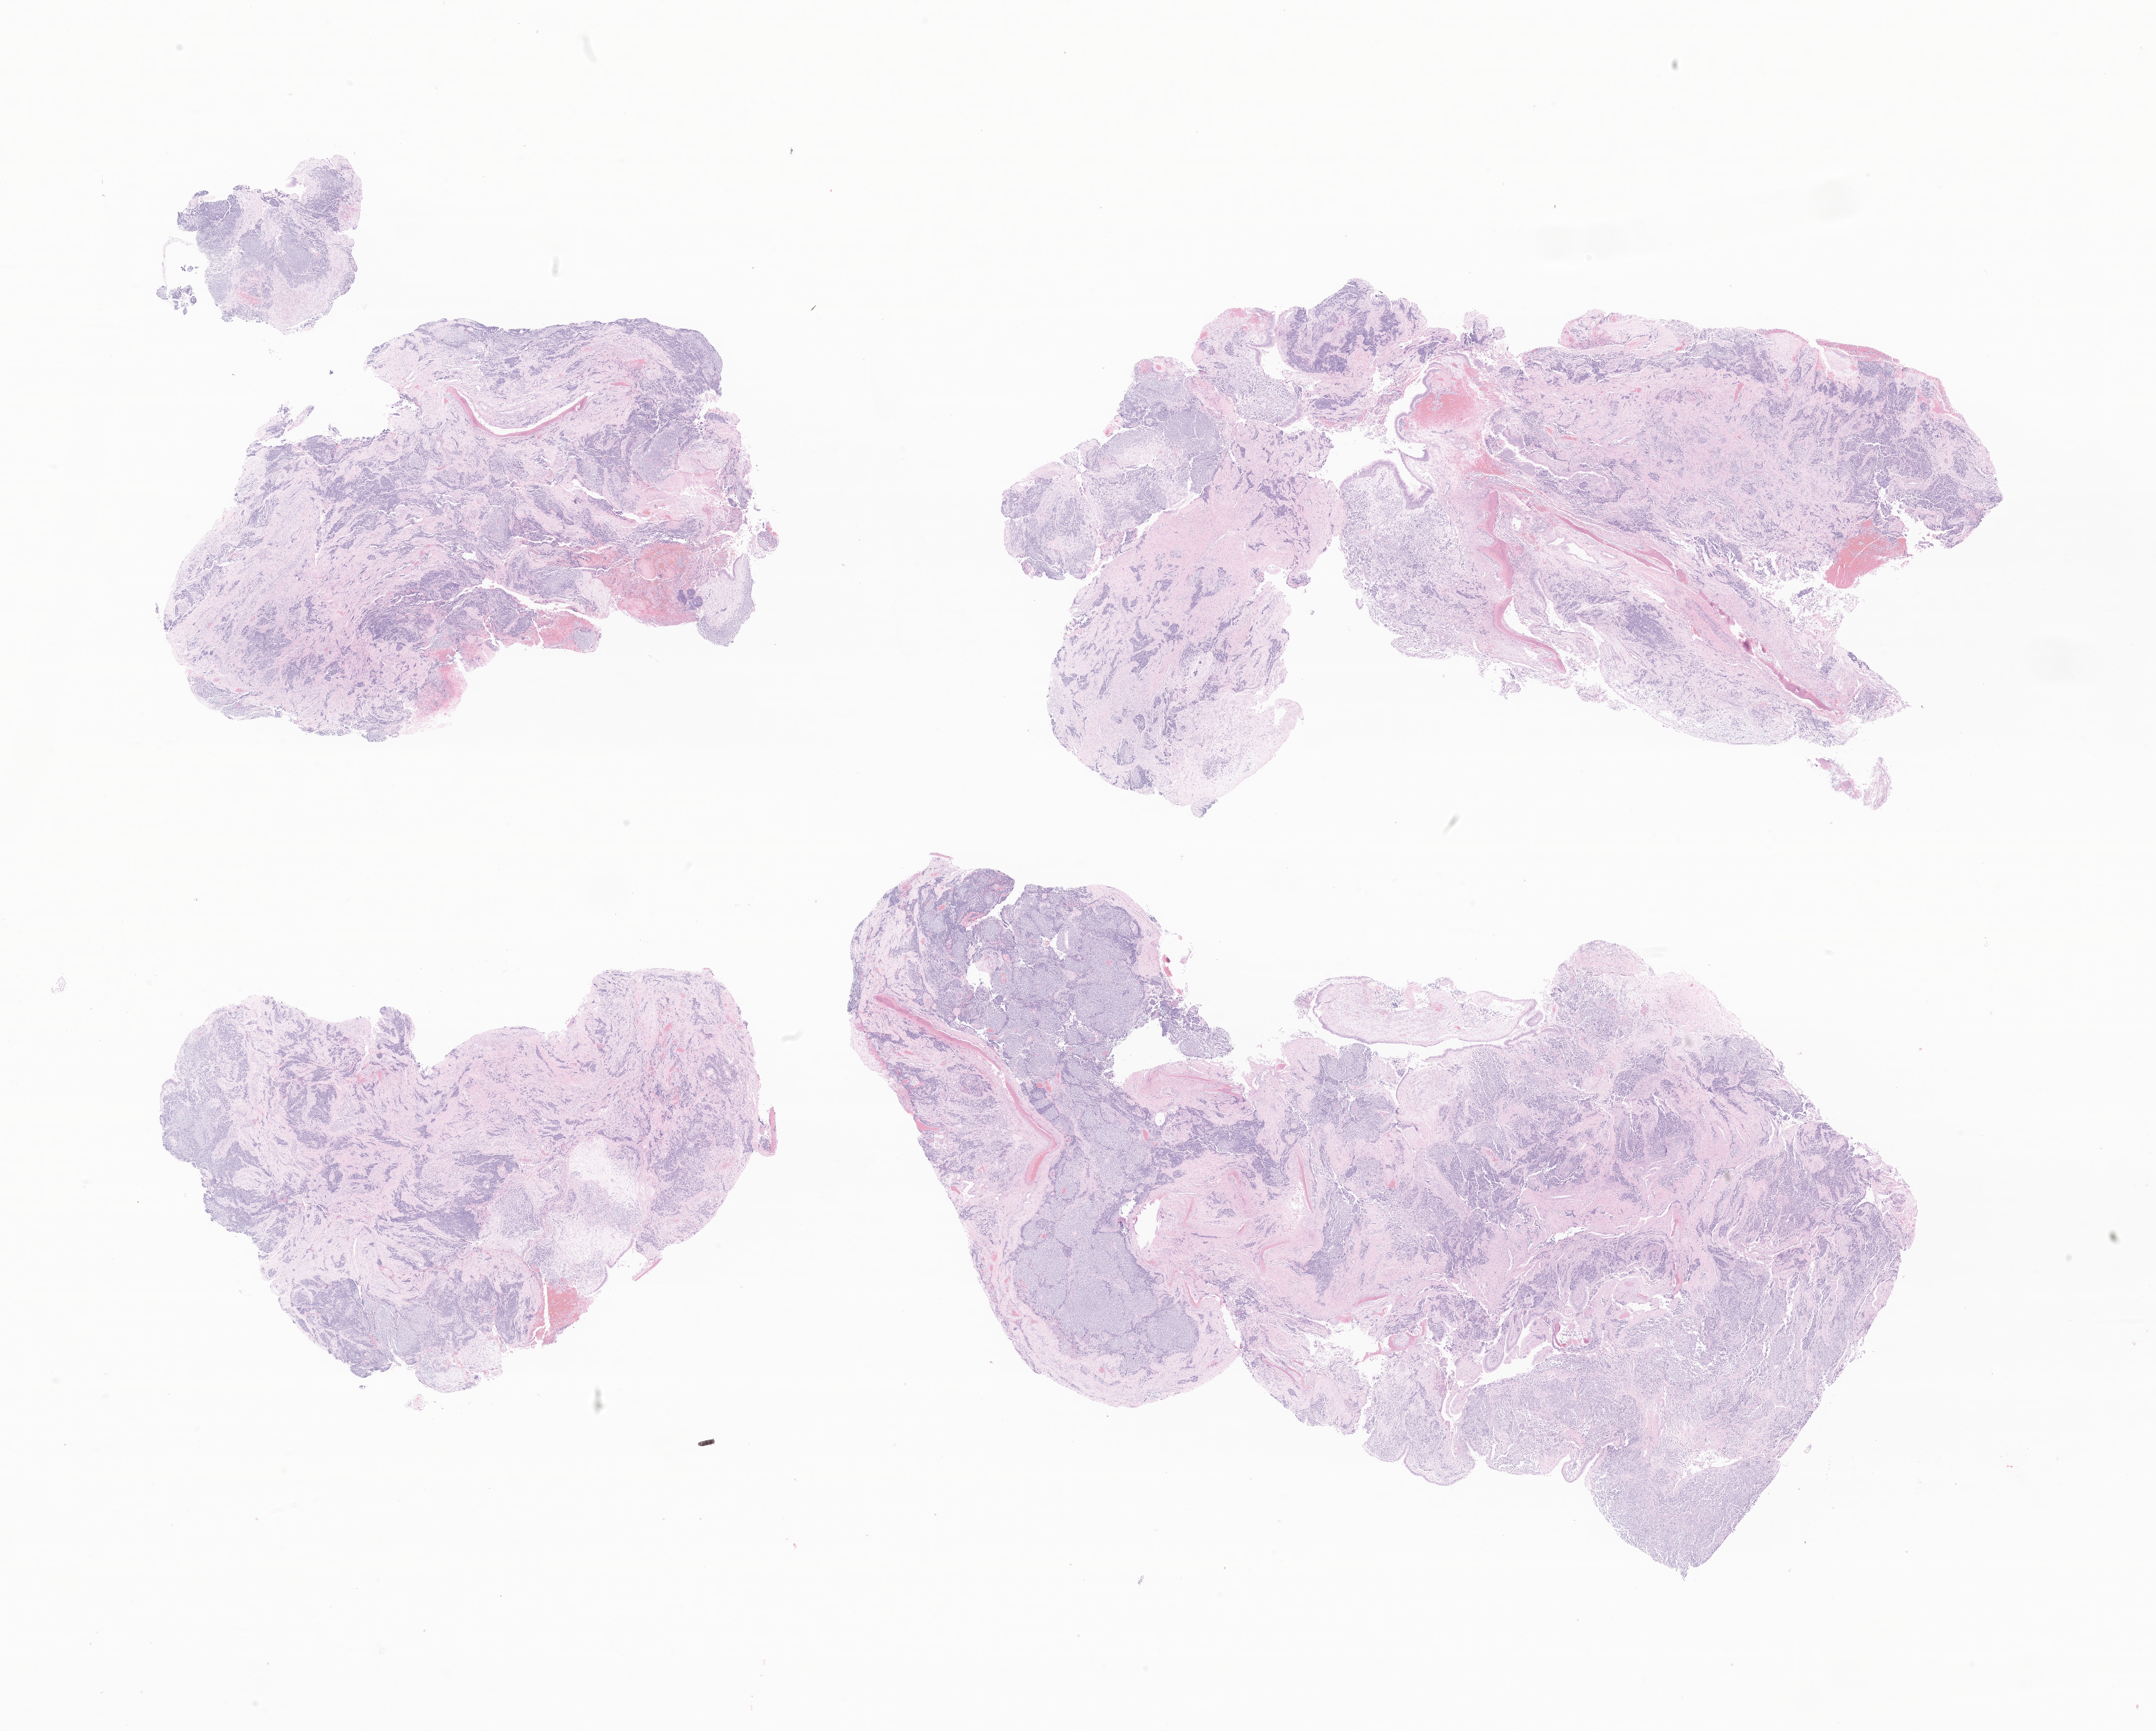
Whole-slide image, hematoxylin and eosin (H&E) stain of tumor tissue from the nasal cavity, shown as a low-resolution overview of the whole scanned area (about 25.7 x 20.6 mm), formalin-fixed paraffin-embedded section. Male patient, age 212 months (17 years 8 months).
Recorded diagnosis: Rhabdomyosarcoma, NOS.